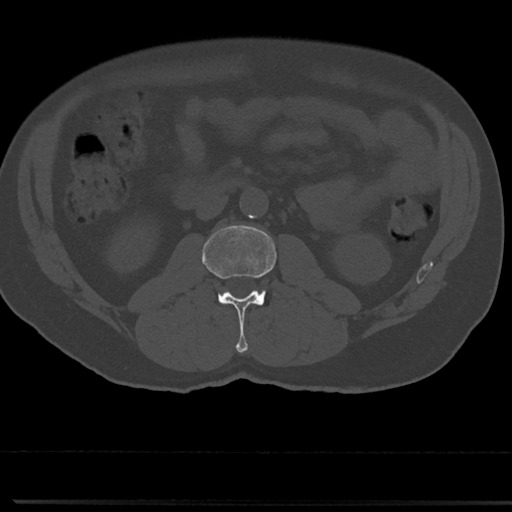
CT including the spine, one axial slice; slice 2 of 817 in the series (ordered by position); bone window (W 1800 / L 400 HU); 512 × 512 image matrix, field of view 355 × 355 mm. Male patient, age 61 years. From the clinical record (not read from this slice): primary cancer: prostate.
Structures marked on this image (semi-automatic segmentation, software-assisted and operator-edited):
- L2 vertebra: box from (x=202, y=225) to (x=276, y=352) px